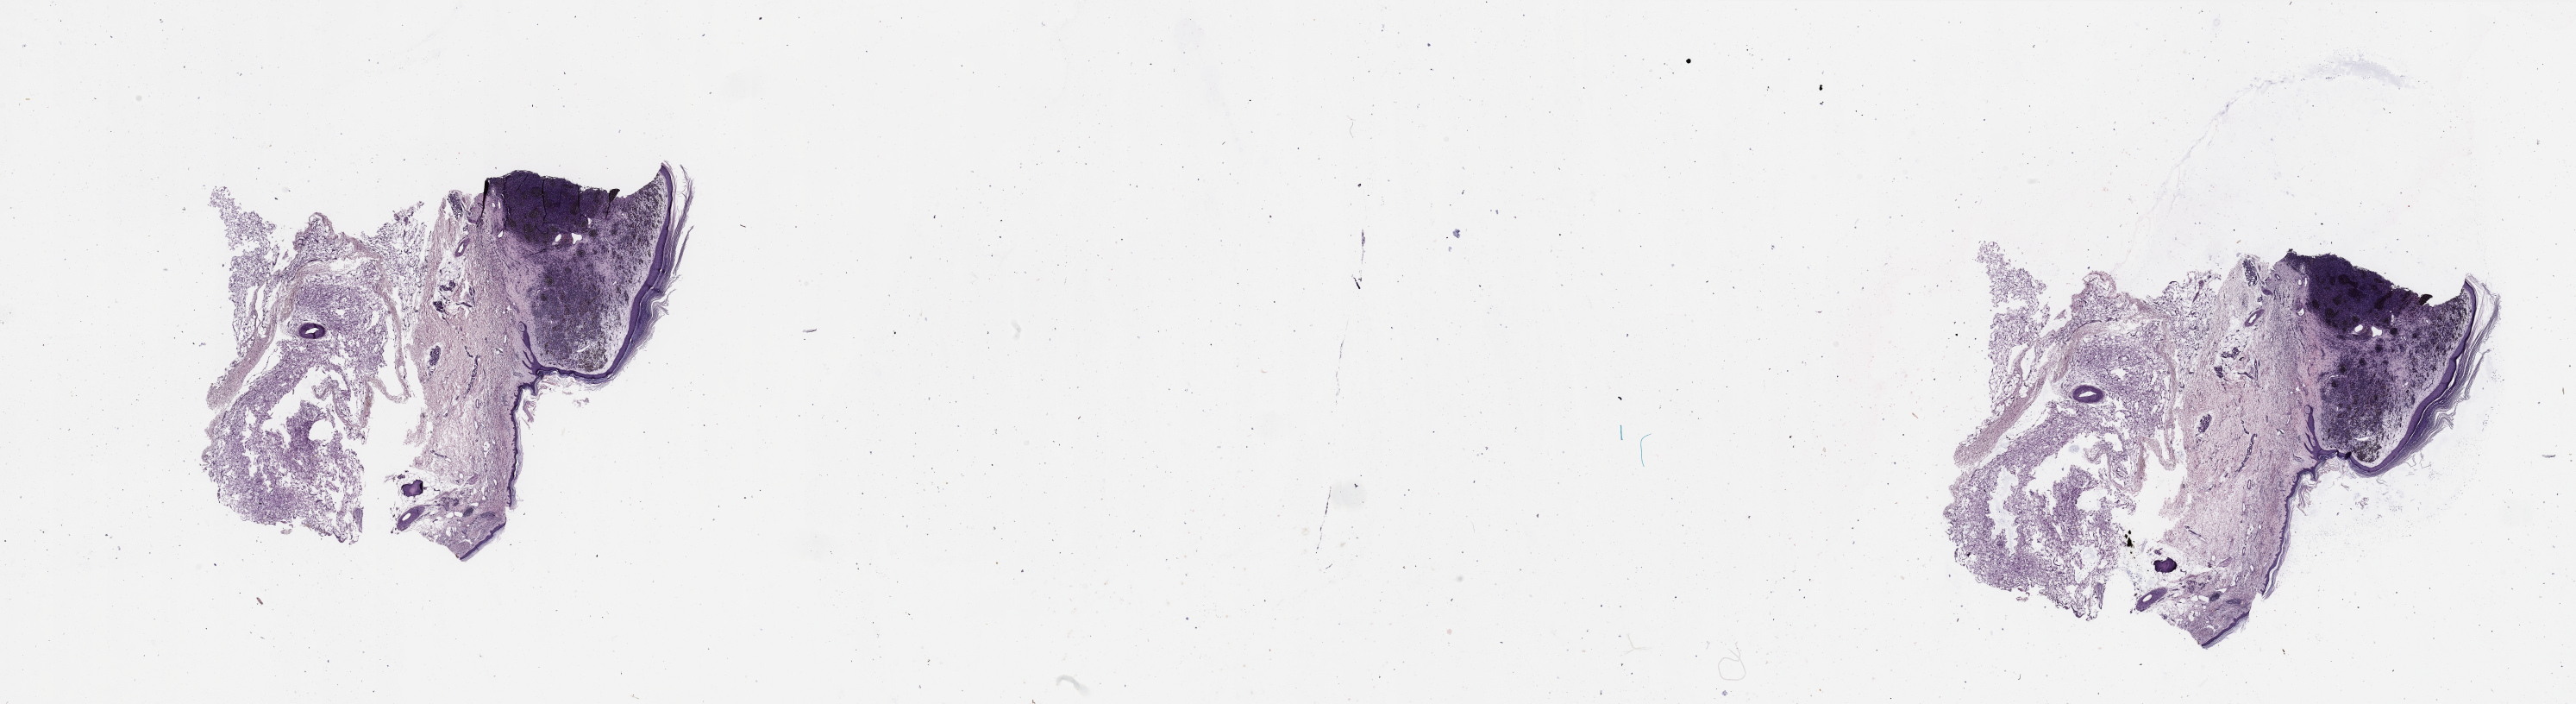
Whole-slide histology image, H&E, a low-resolution overview of the entire scanned area, about 47.3 x 12.9 mm (slide scanned at 20x), melanoma tumour tissue; sampled site not recorded. Patient: female, age 78 years.
AJCC pathologic stage: IIB. Diagnosis: Malignant melanoma, NOS. Primary tumour site (as recorded): extremities.